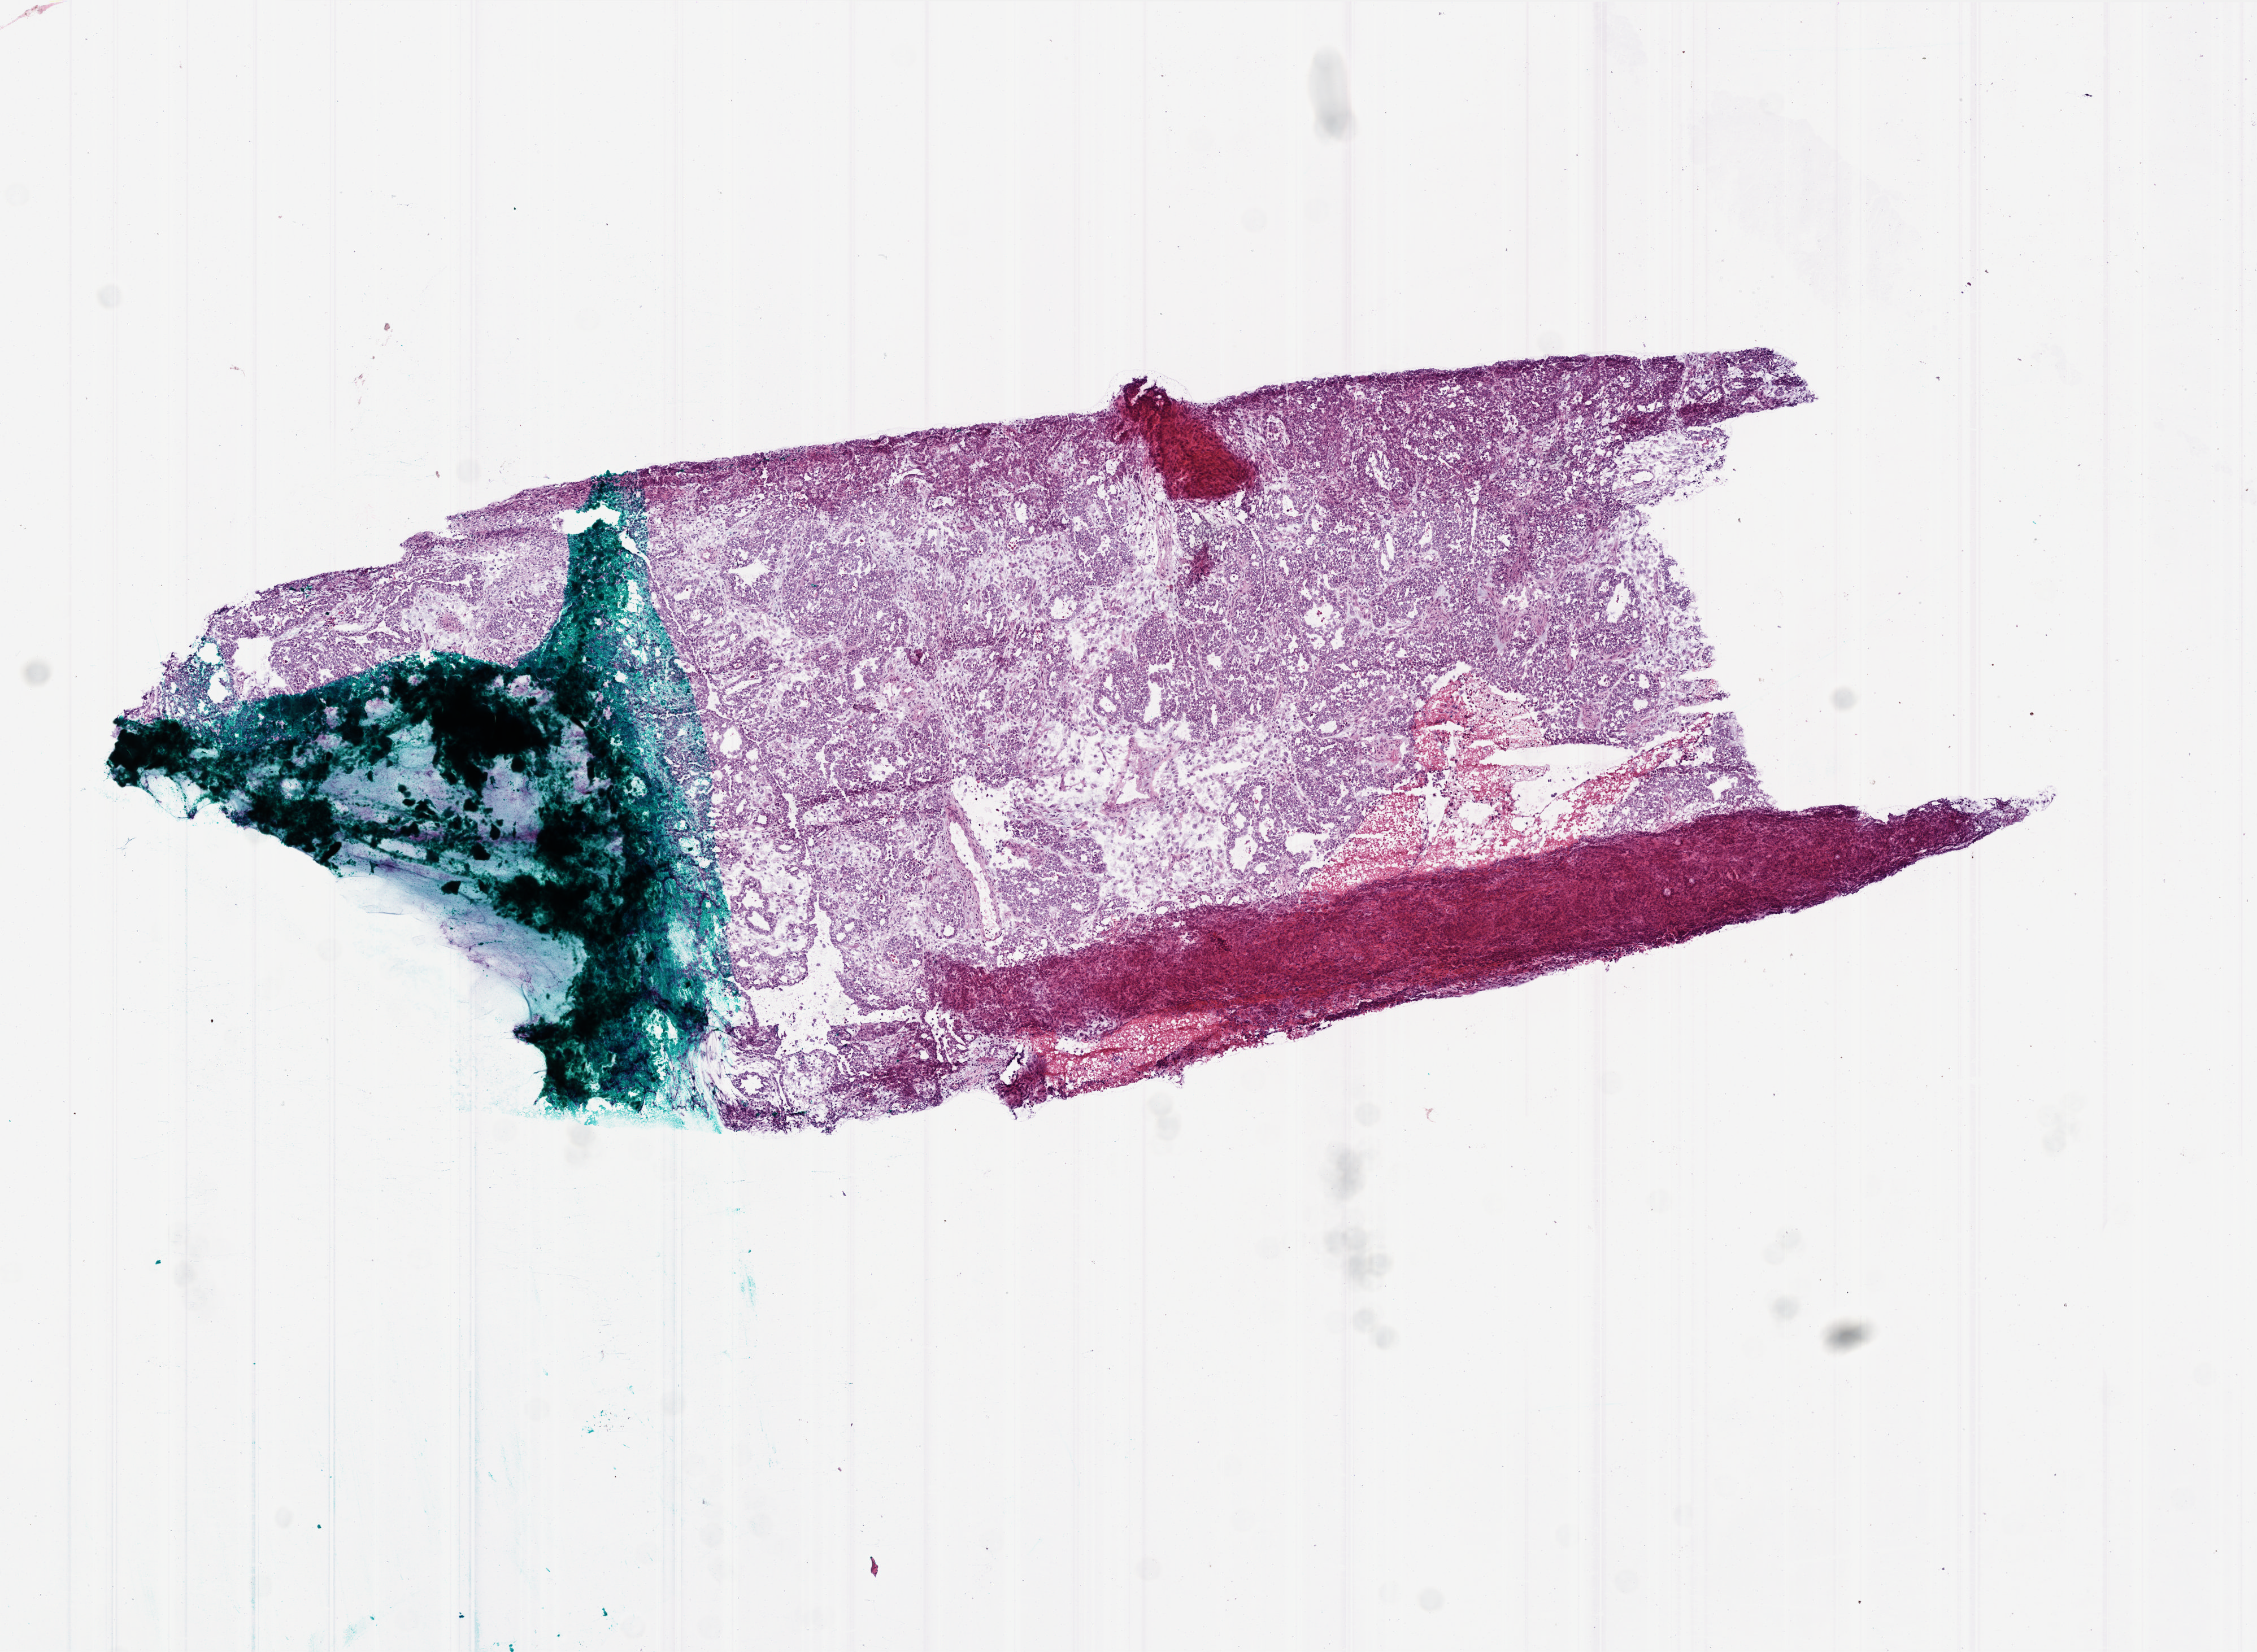
Whole-slide histology image, H&E, a low-resolution overview of the entire scanned area, about 8.0 x 5.9 mm (acquisition: 20x scan), frozen section, sample: primary tumour, ovary. Female patient; age at initial diagnosis 56 years. Histologic grade: G3 (poorly differentiated). Composition of this section per pathologist review: tumour cells 95%, tumour nuclei 98%, normal cells 0%, stromal cells 5%, necrosis 0%.
* diagnosis: Serous cystadenocarcinoma, NOS
* laterality: left
* FIGO stage: IIIC